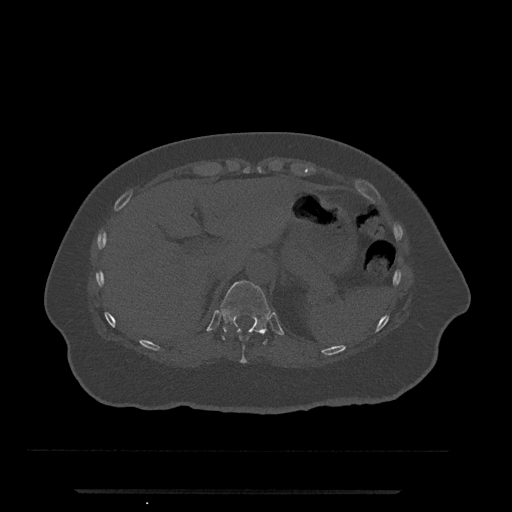
CT including the spine, one axial slice; position 247 of 797 along the scan axis; reconstruction kernel Br40s/3; 120 kVp; bone window (W 1800 / L 400 HU); 0.5 mm slice thickness; 512 × 512 image matrix, field of view 440 × 440 mm. Patient: female, 51 years. From the clinical record (not read from this slice): primary cancer: neuro.
Annotated regions visible in this slice (semi-automatically segmented with operator editing):
- T10 vertebra: bounding box (x1, y1, x2, y2) in pixels: (239, 338, 248, 364)
- T11 vertebra: (214, 281, 271, 345)